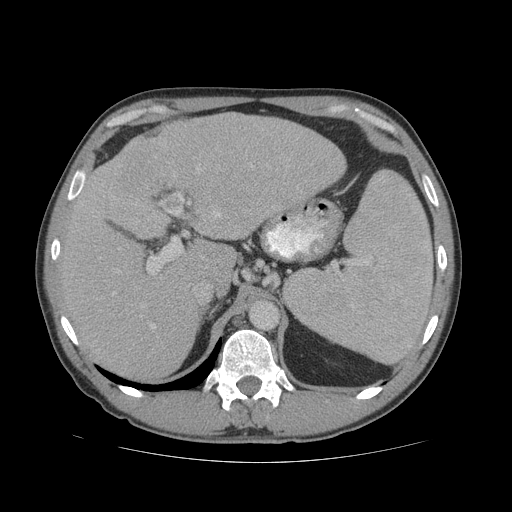
Contrast-enhanced abdominal CT (liver protocol), one axial slice. Position 44 of 81 along the scan axis. Reconstruction kernel STANDARD. Soft-tissue window (W 400 / L 40 HU). 2.5 mm slice thickness. 512 × 512 image matrix. Case-level facts recorded for this patient, not image findings: diagnosis: hepatocellular carcinoma (patient treated with transarterial chemoembolisation; whether this scan precedes or follows treatment is not stated here); TNM stage (as recorded): Stage-IVB; Child-Pugh class: B; tumour differentiation: well differentiated; tumour nodularity: multinodular.
Annotated regions visible in this slice (semi-automatically segmented with operator editing):
- liver parenchyma outside the tumour (the mass and vessels are separate outlines, so this box may not span the whole liver): bounding box [x1, y1, x2, y2] px = [56, 112, 346, 380]
- mass: [112, 139, 171, 200]
- liver vessels: [112, 165, 253, 329]